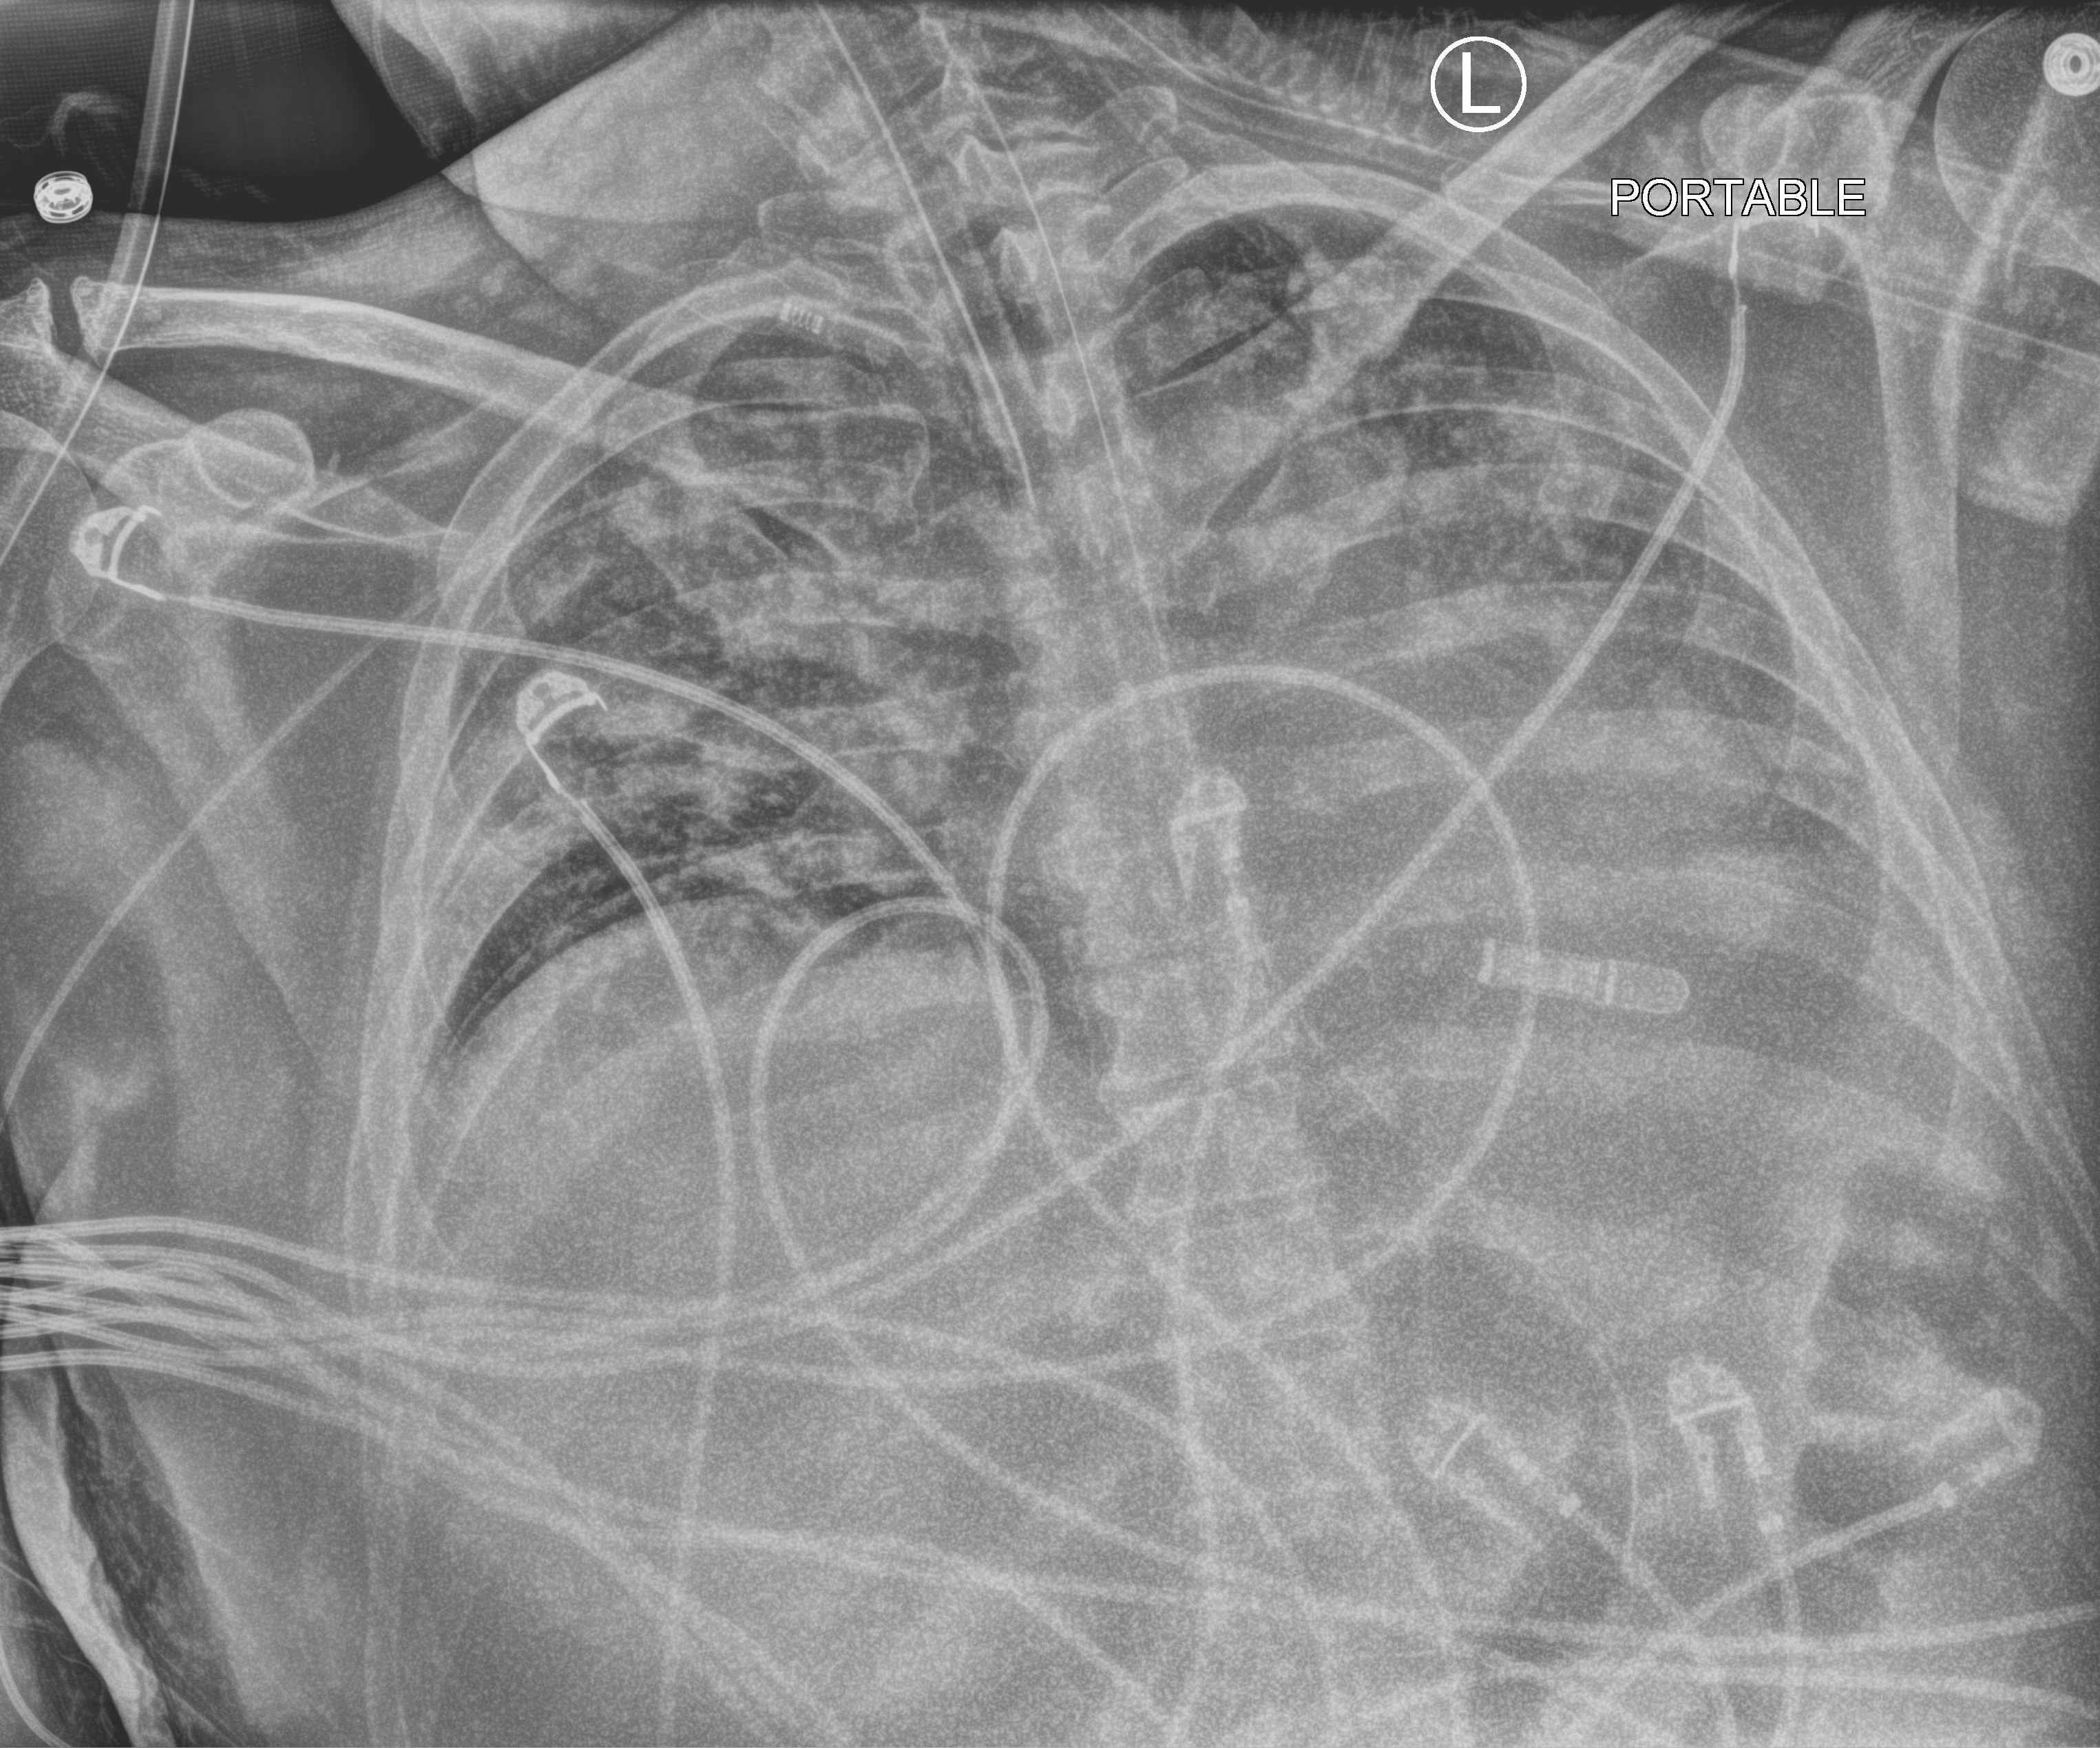
Bedside chest radiograph (computed radiography), anteroposterior (AP) projection. Patient hospitalised with COVID-19; male, aged 18–59 years.
Admission-level facts for this patient (not findings on this image; timing relative to this image not recorded): admitted to intensive care during this hospital stay: yes; length of hospital stay: 39 days.